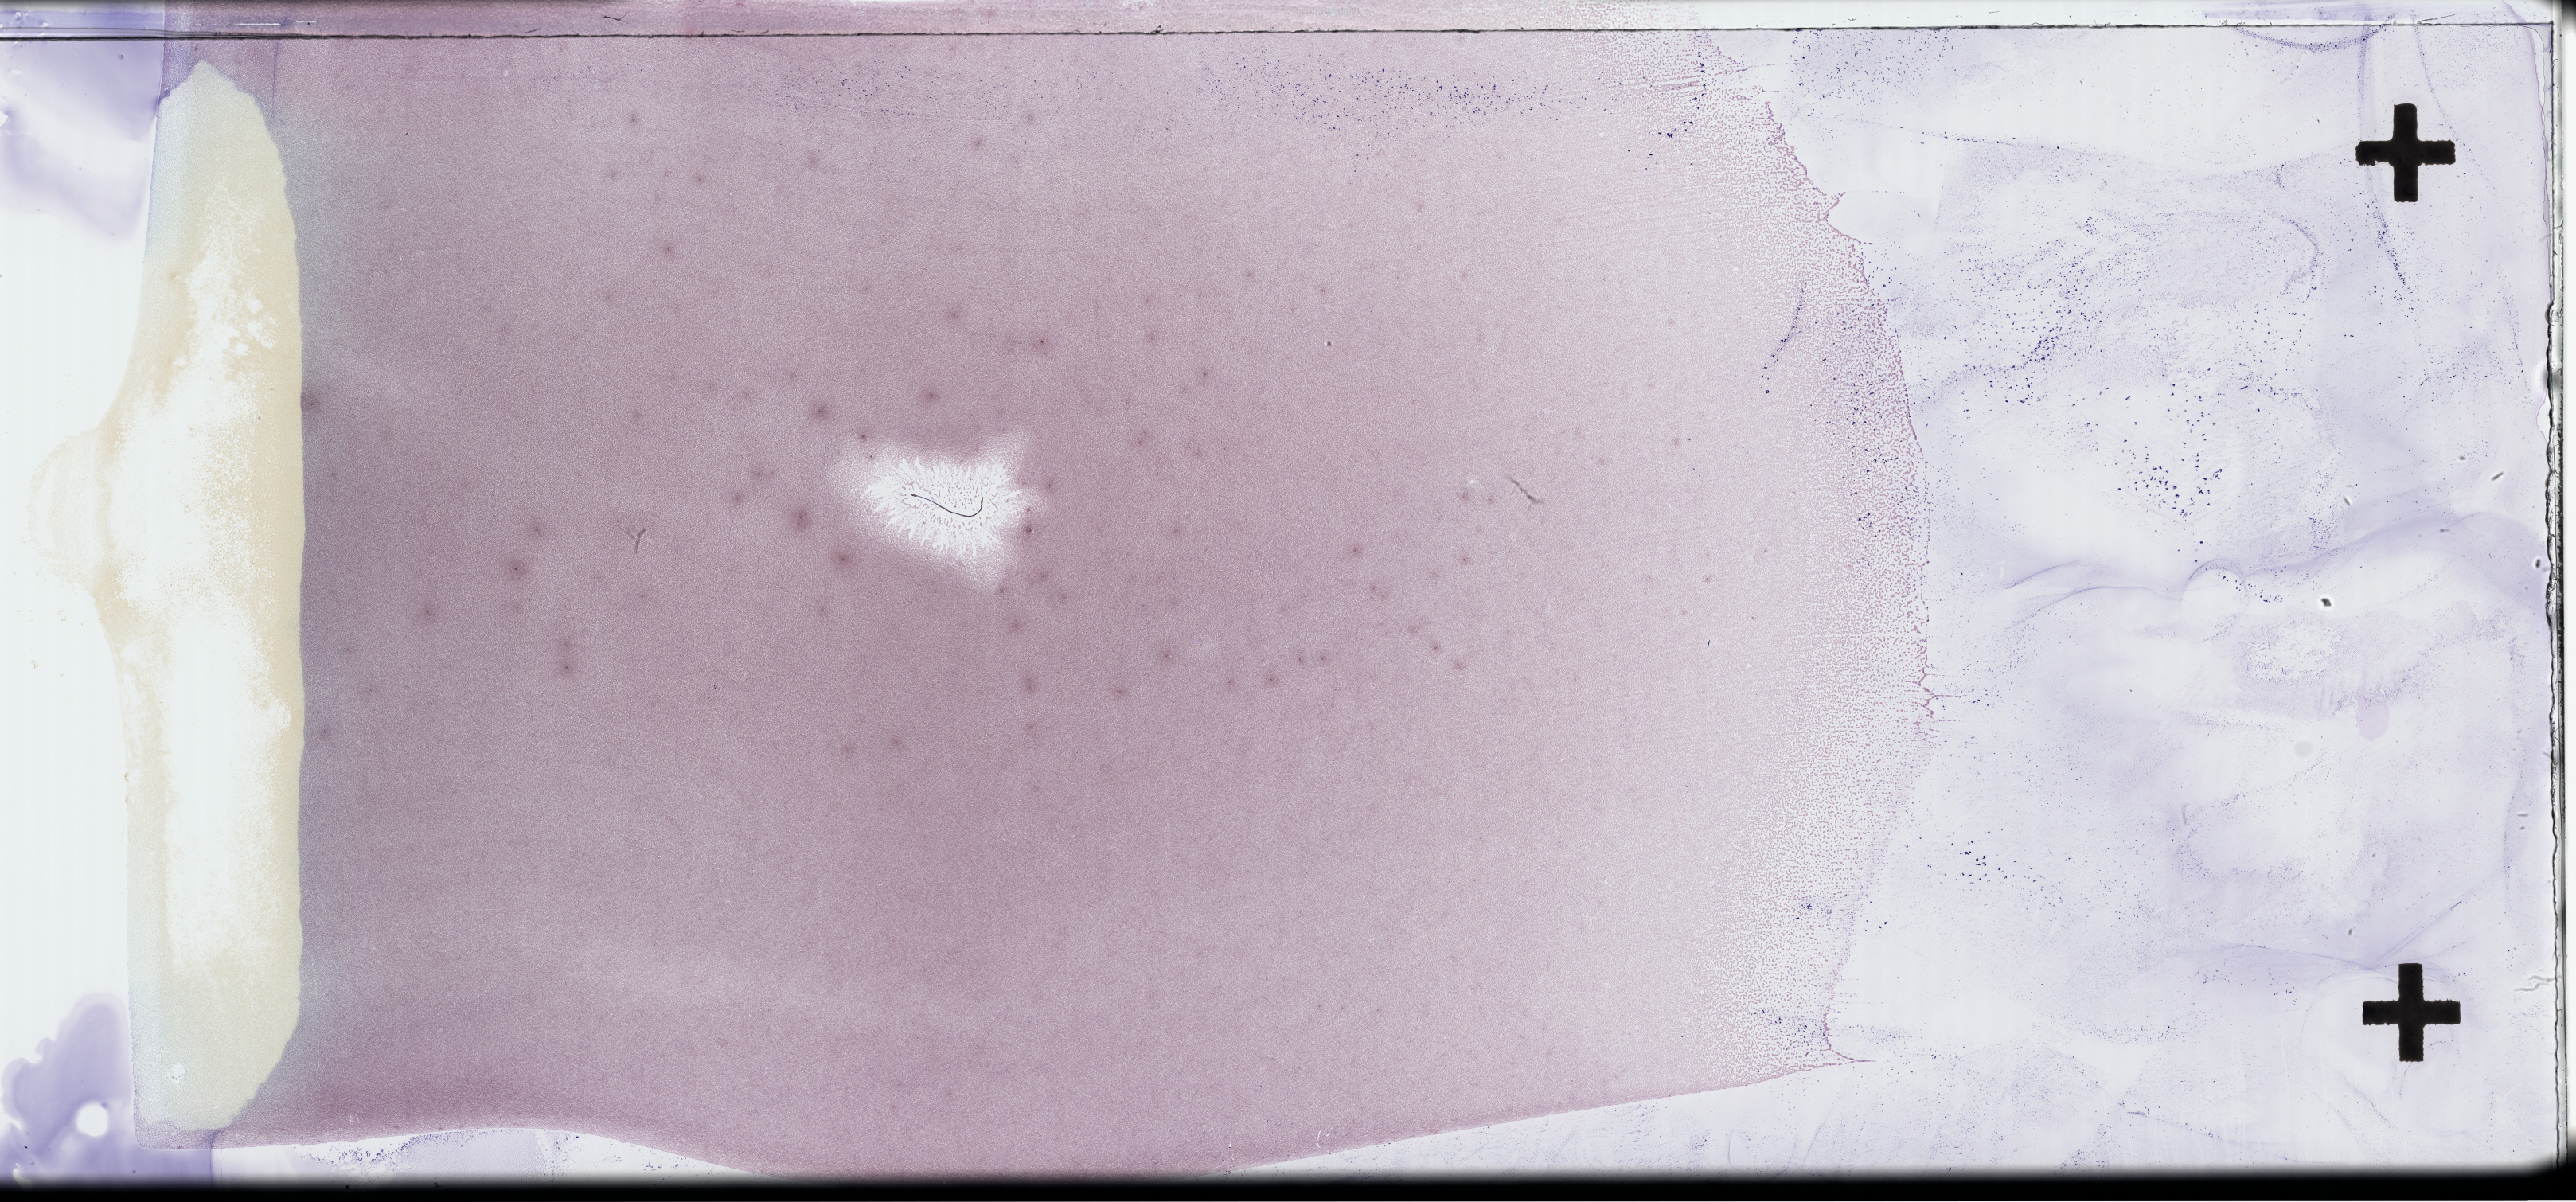
Whole-slide image of a bone marrow smear, Wright–Giemsa stain, low-resolution overview of the scanned area, about 52.3 x 24.4 mm. Specimen time point: collected at baseline (before treatment). Patient sex: female.
From a patient with: Plasma Cell Myeloma.